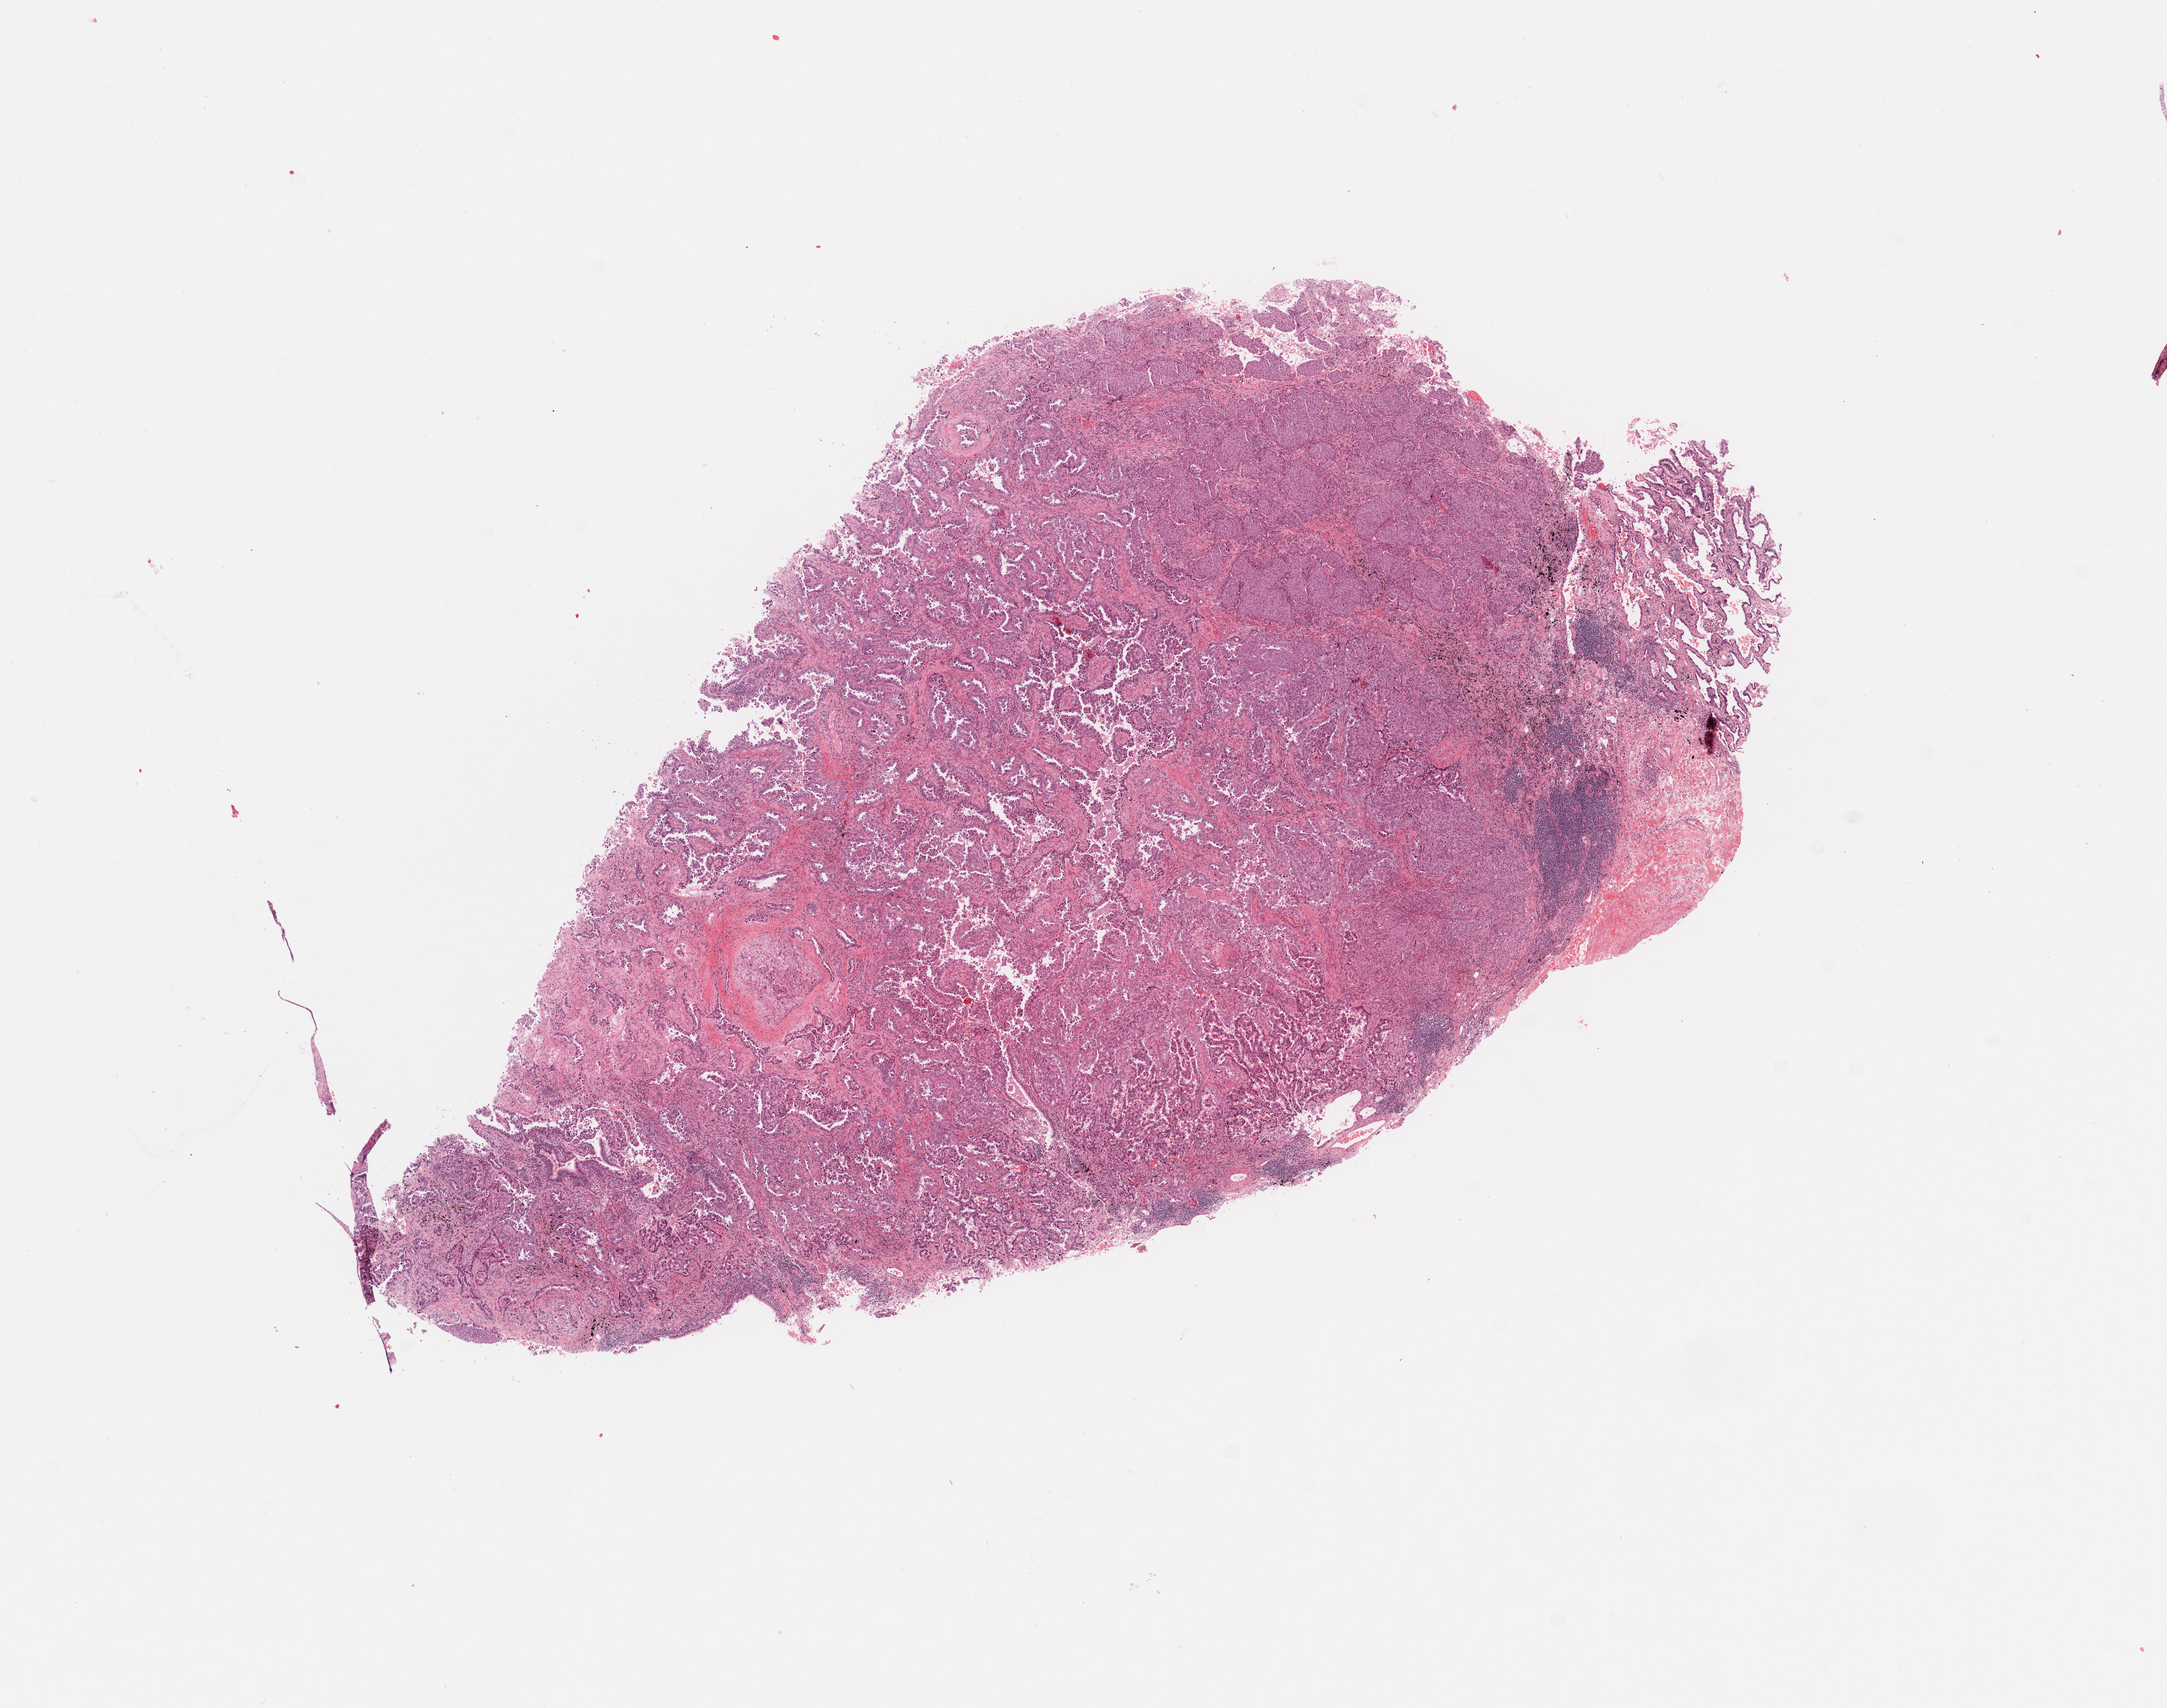
H&E-stained whole-slide image — shown as a low-resolution overview of the whole scanned area (about 14.8 x 11.6 mm). Tumour tissue sample, sampled site: lung. Male, 77 y/o. Histologic grade: G3 (poorly differentiated). Slide review estimates, as recorded: tumour nuclei 80%, necrosis 5%.
Primary tumour site (as recorded): left upper lobe. Histologic diagnosis: Adenocarcinoma, NOS. AJCC pathologic stage: IIB.